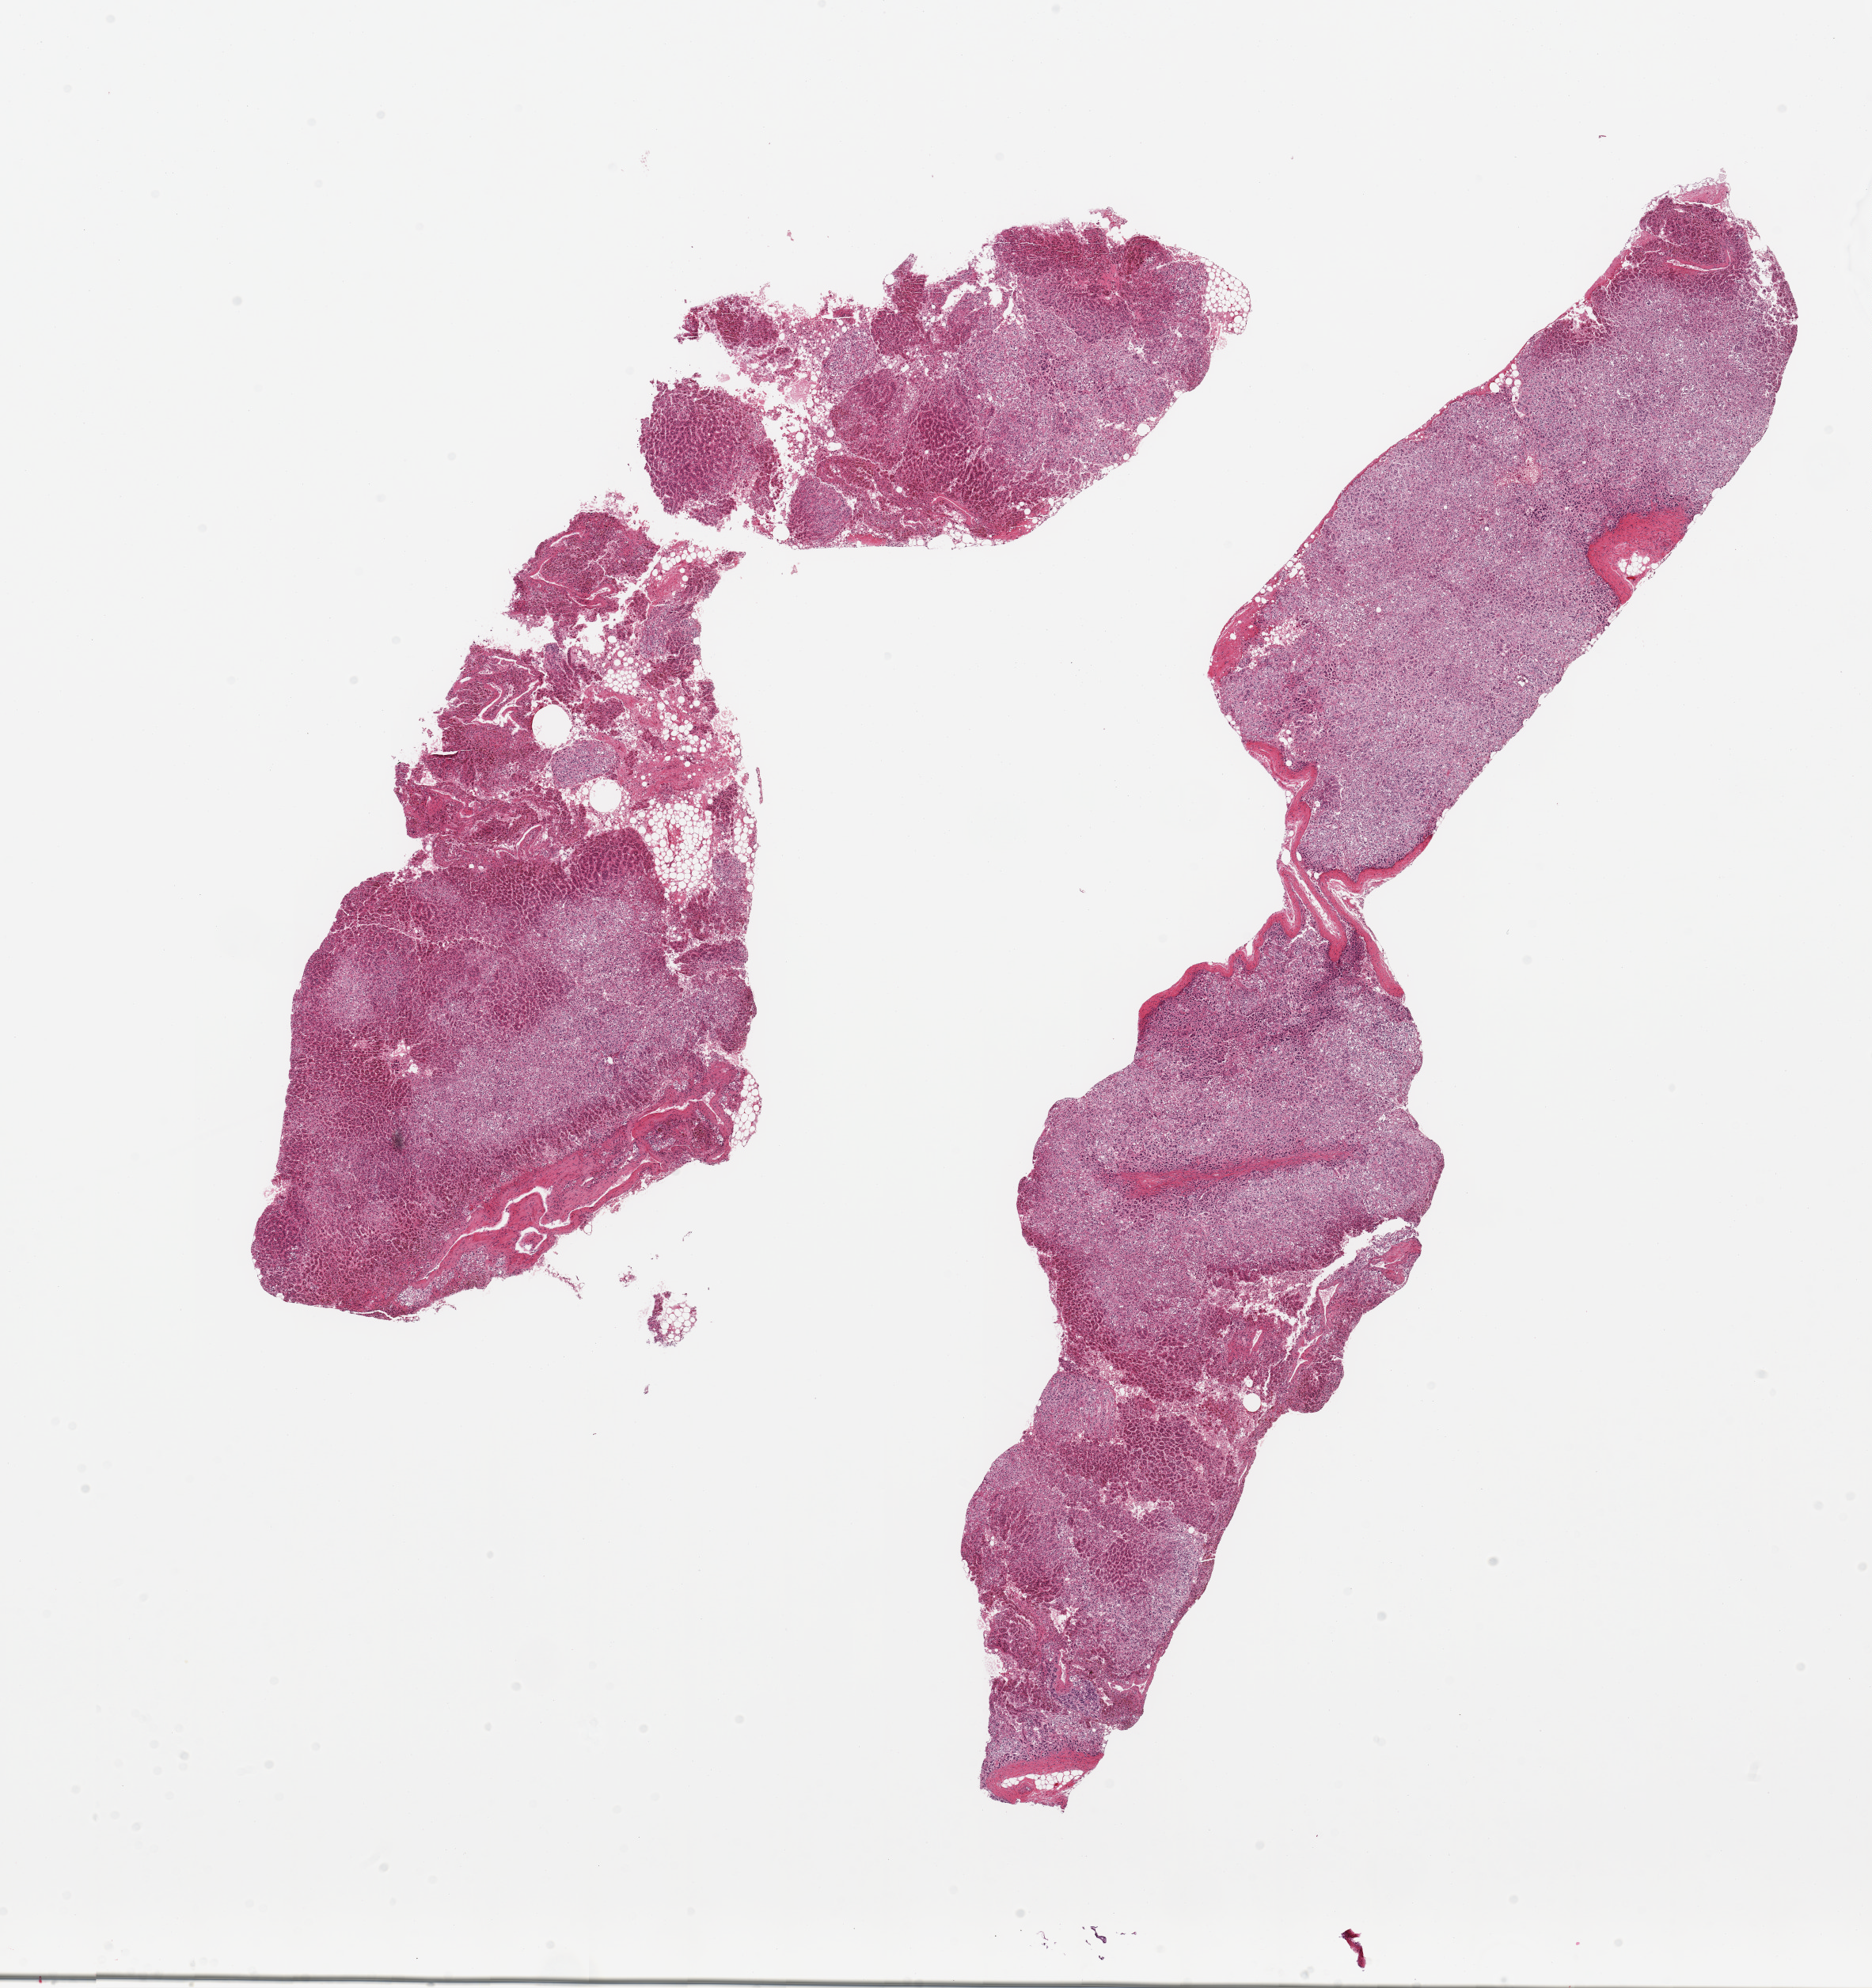
Digitized H&E-stained section, whole scanned area (about 18.7 x 19.9 mm) shown as a low-resolution overview; PAXgene-fixed, paraffin-embedded tissue; target tissue: adrenal gland; donor tissue sample. Donor: male.
- review note (as recorded): 2 partially fragmented pieces; 20% fat in 1 piece